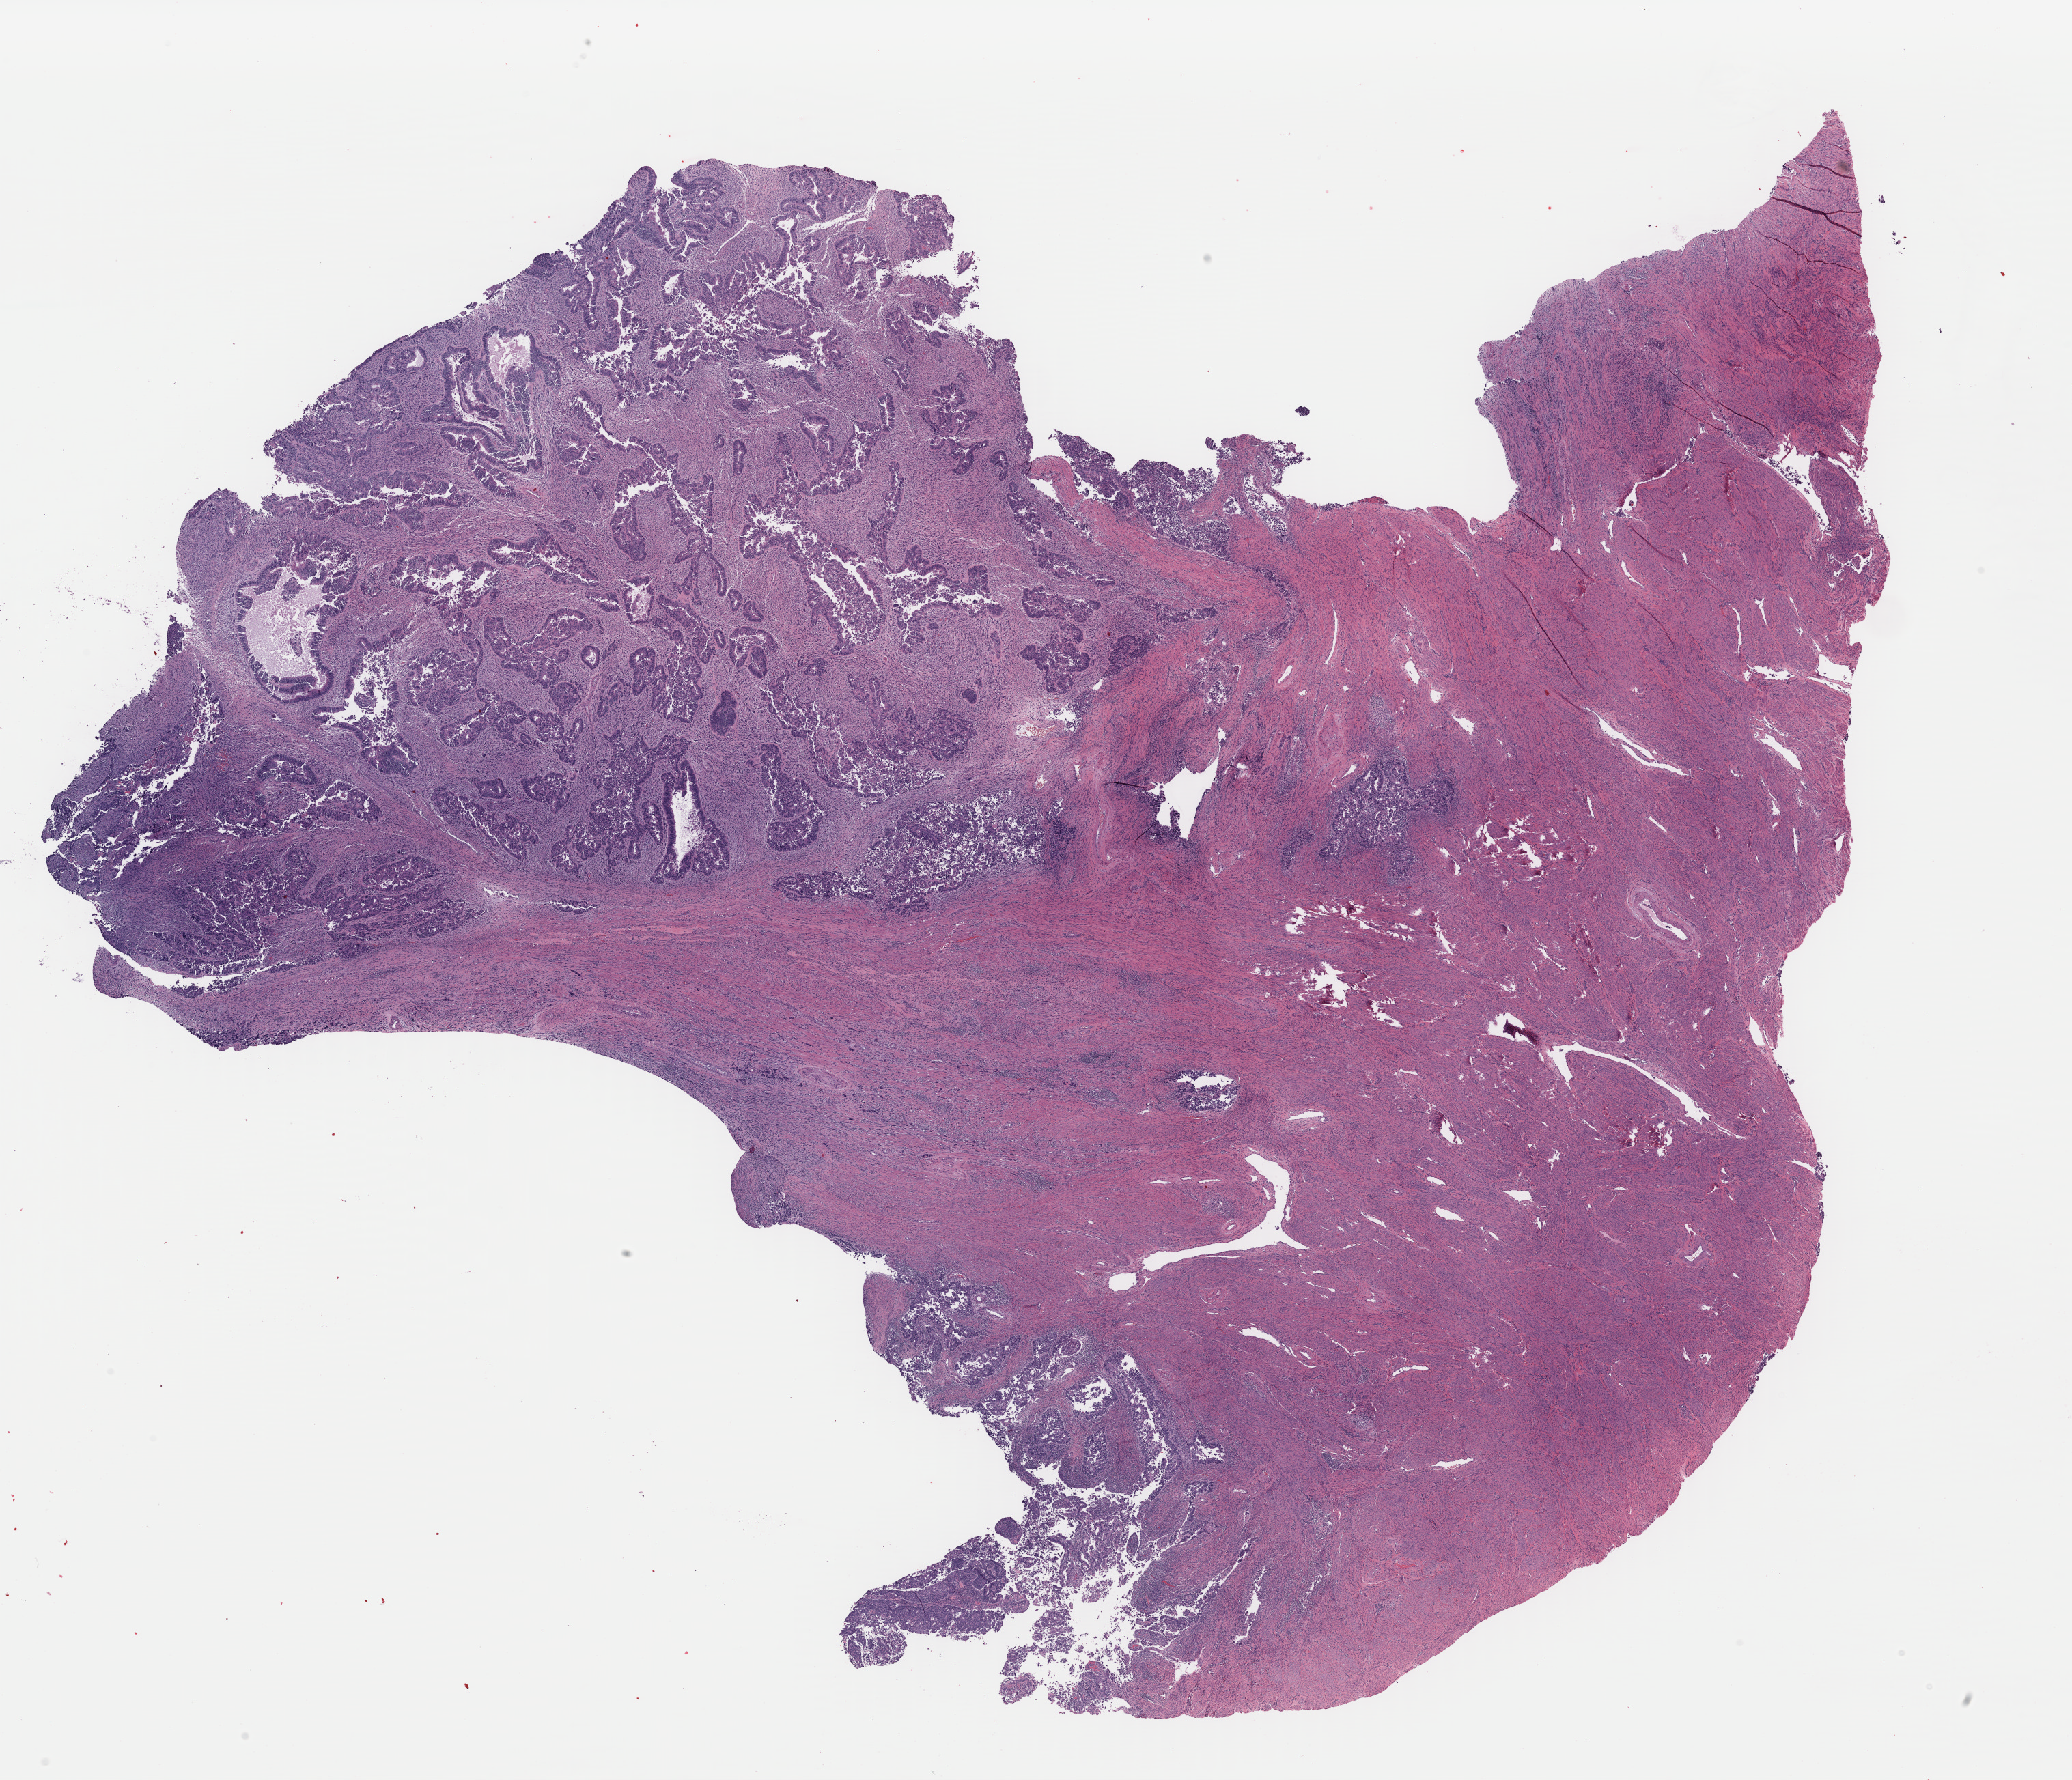
H&E-stained whole-slide image, whole scanned area (about 23.9 x 20.6 mm, acquisition: 40x scan) shown as a low-resolution overview. Formalin-fixed paraffin-embedded (FFPE) diagnostic section. Primary tumour sample from the uterus. Patient: female, age at initial diagnosis 51 years.
- diagnosis: Mullerian mixed tumor
- FIGO stage: IB